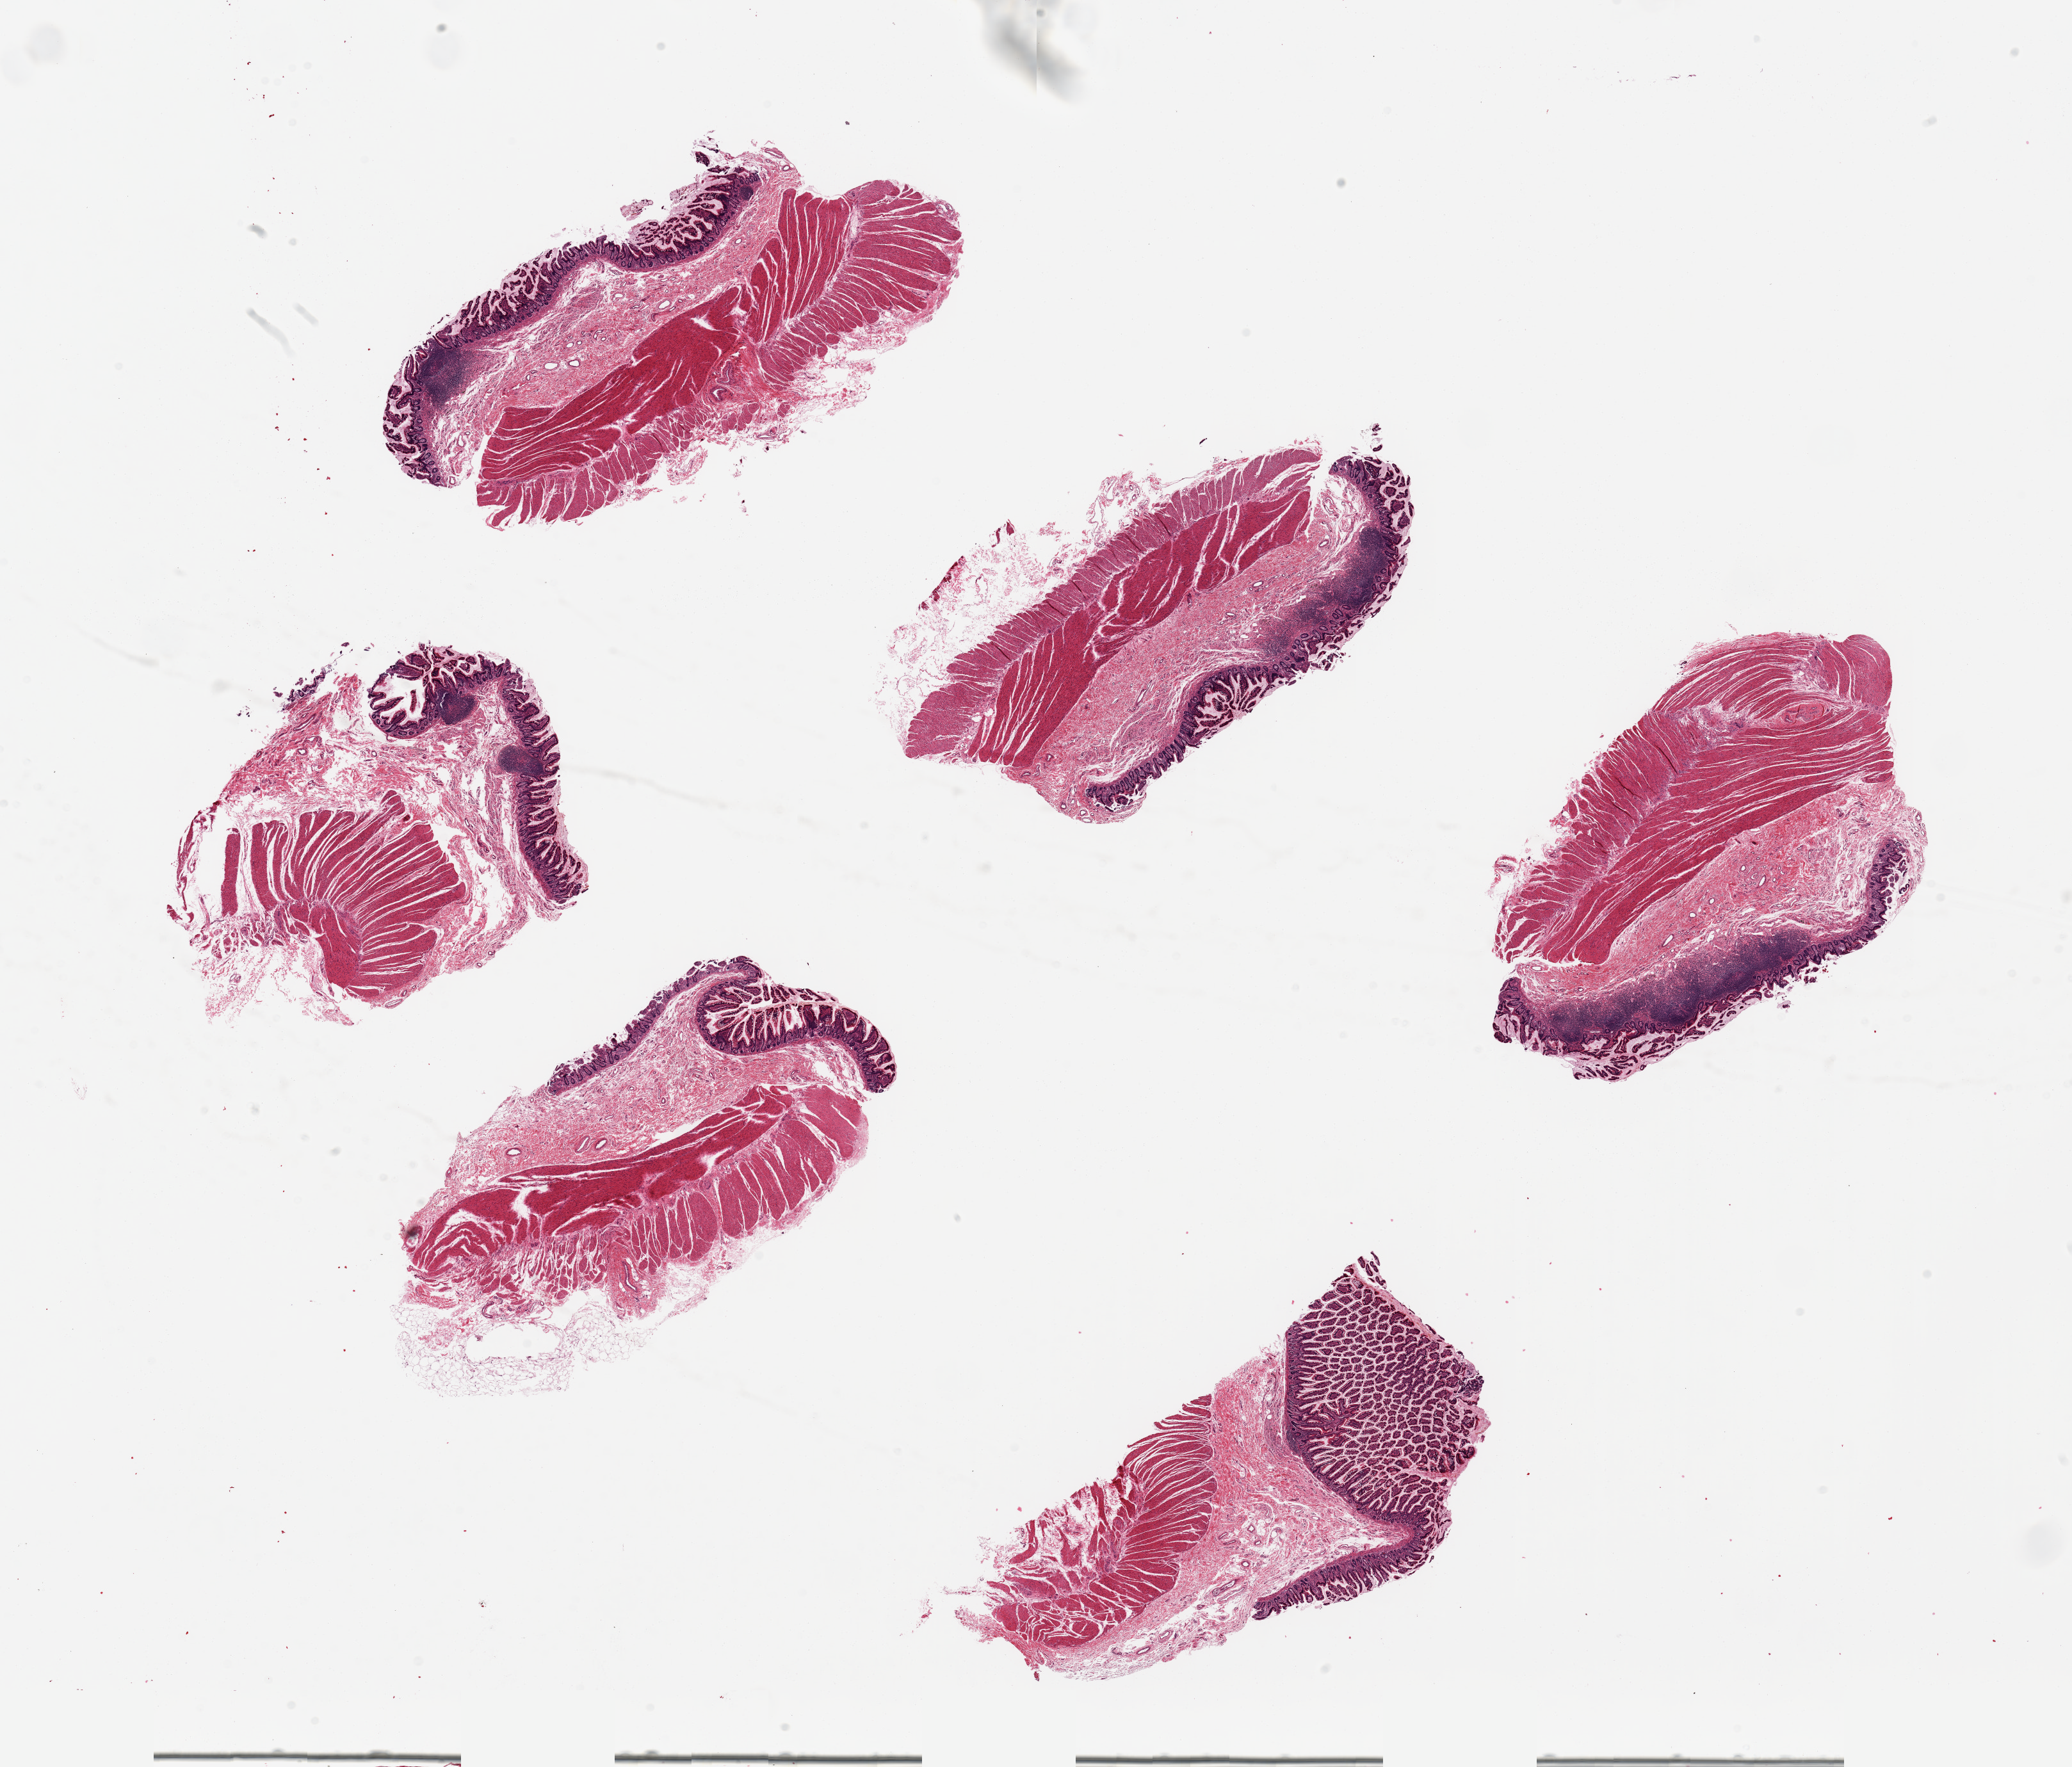
Whole-slide image, hematoxylin and eosin (H&E) stain — whole scanned area (about 25.6 x 21.8 mm, from a 20x scan) shown as a low-resolution overview, PAXgene-fixed paraffin-embedded (PFPE) section, sampled site (target tissue): ileum, tissue donor sample.
Pathologist's review note for this sample: 6 pieces, exceptionally well-preserved; lymphoid aggregates ~10-15% of total tissue.